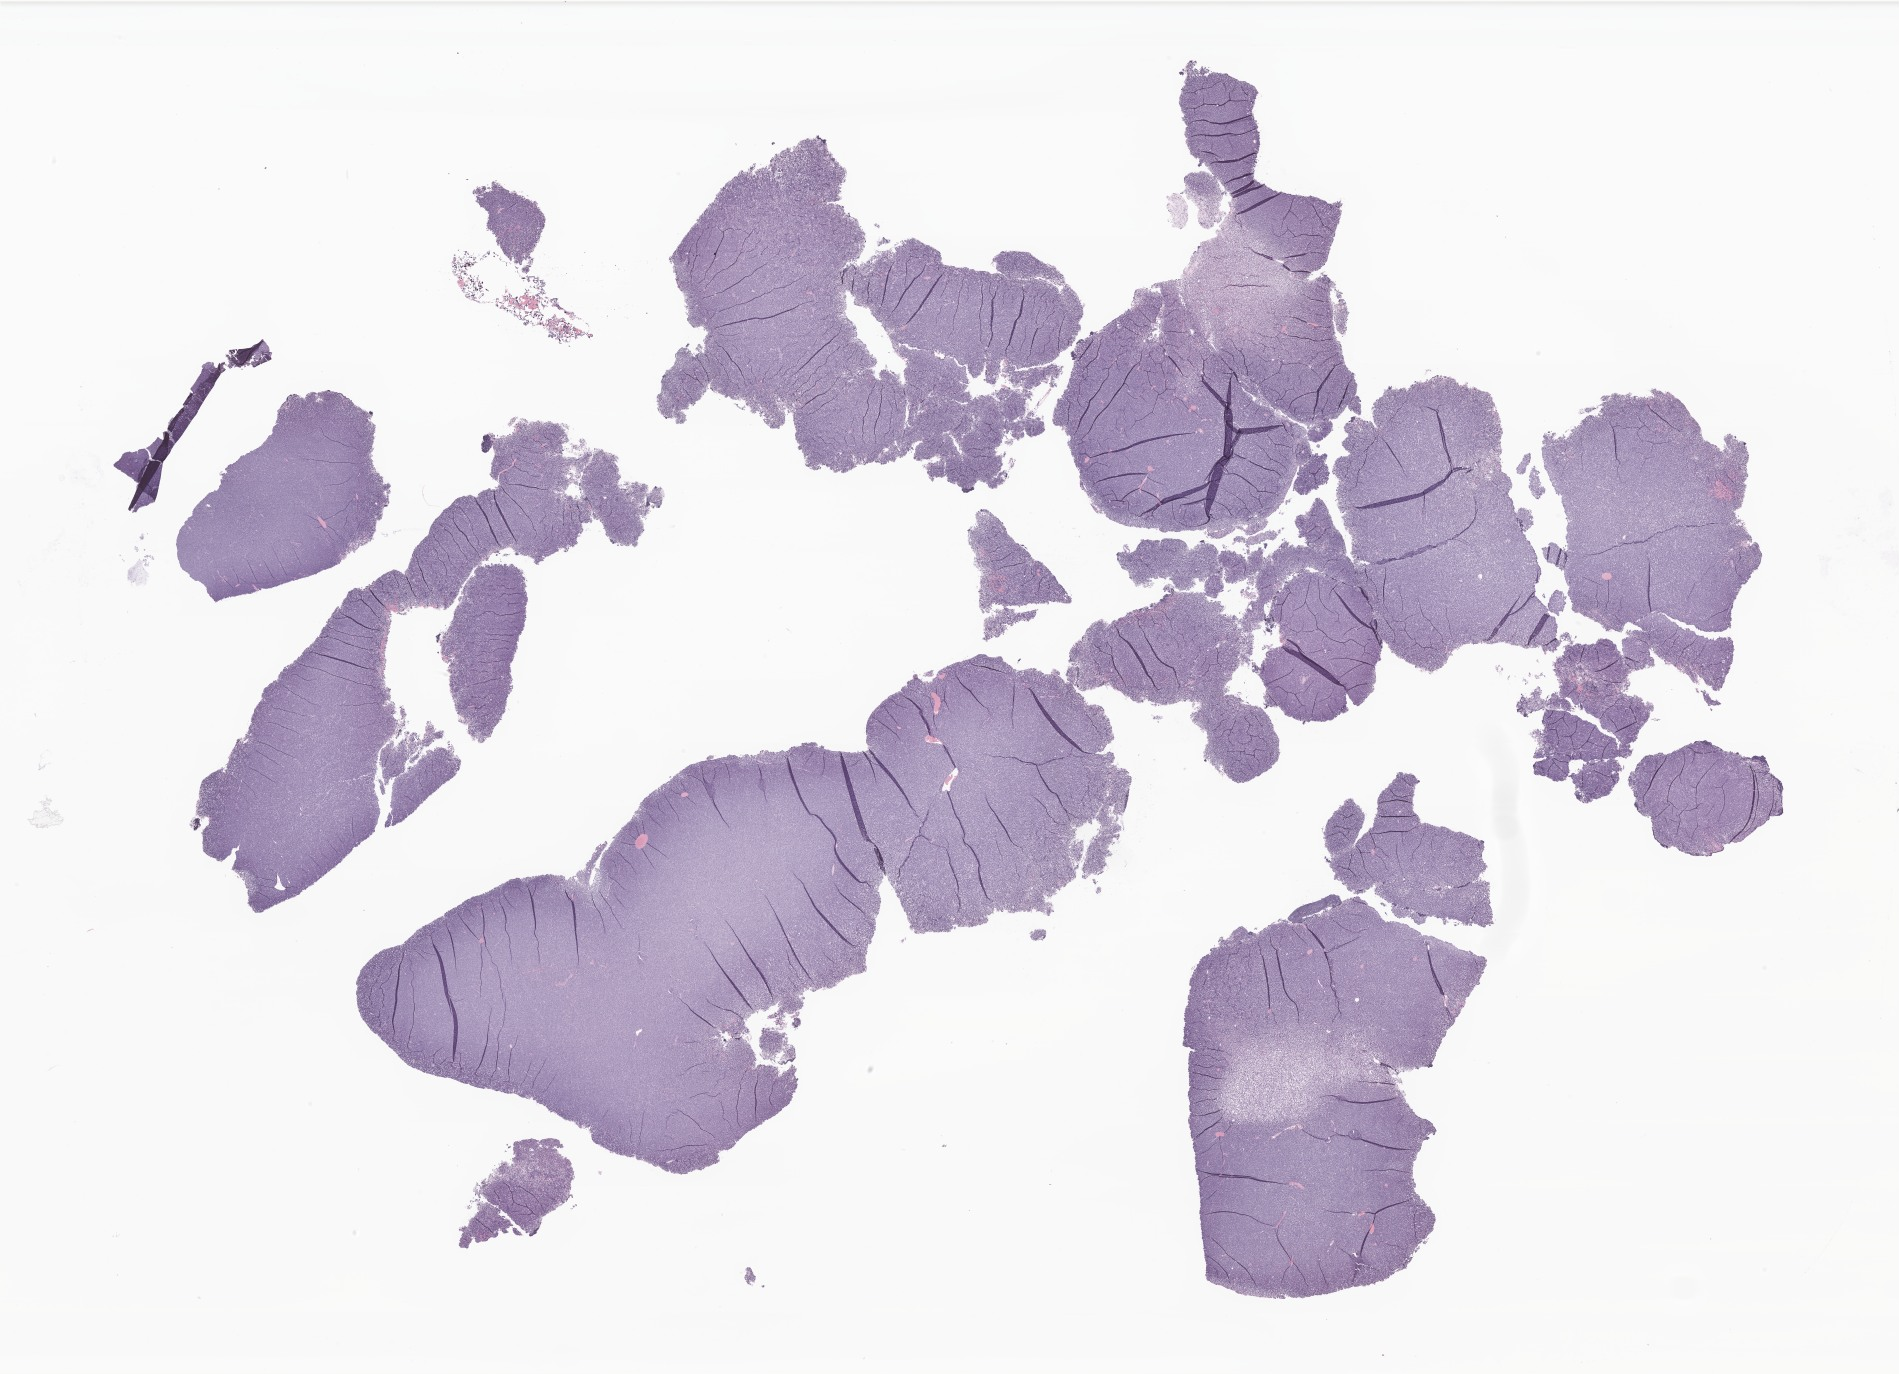
Digitized hematoxylin and eosin (H&E)-stained section of tumor tissue from the brain — whole scanned area (about 32.0 x 23.2 mm) shown as a low-resolution overview, formalin-fixed paraffin-embedded section. Patient male; age 211 months (17 years 7 months).
Recorded diagnosis: Medulloblastoma, NOS.